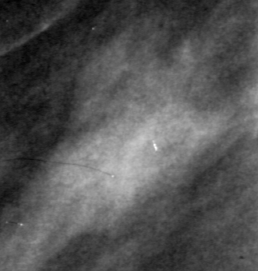
Region of interest cut from a scanned film mammogram (one marked finding); left breast; MLO view; BI-RADS breast density category 1 (scale 1–4).
Mass, shape irregular, margins ill defined; BI-RADS assessment category 4; subtlety rating 2 on a 1 (subtle) to 5 (obvious) scale; pathology result (as recorded, not read from the image): malignant.